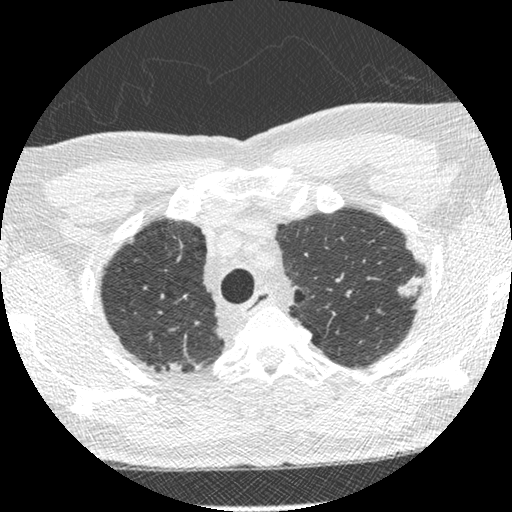
Low-dose screening chest CT, one axial slice. Slice 237 of 275 in the series (ordered by position). 120 kVp. Lung window (W 1500 / L -600 HU). 1.25 mm slice thickness. 512 × 512 image matrix, field of view 330 × 330 mm.
Annotated regions visible in this slice (expert manual segmentation):
- lesion 1 (tumor, upper lobe of left lung): bounding box [x1, y1, x2, y2] px = [398, 276, 422, 296]